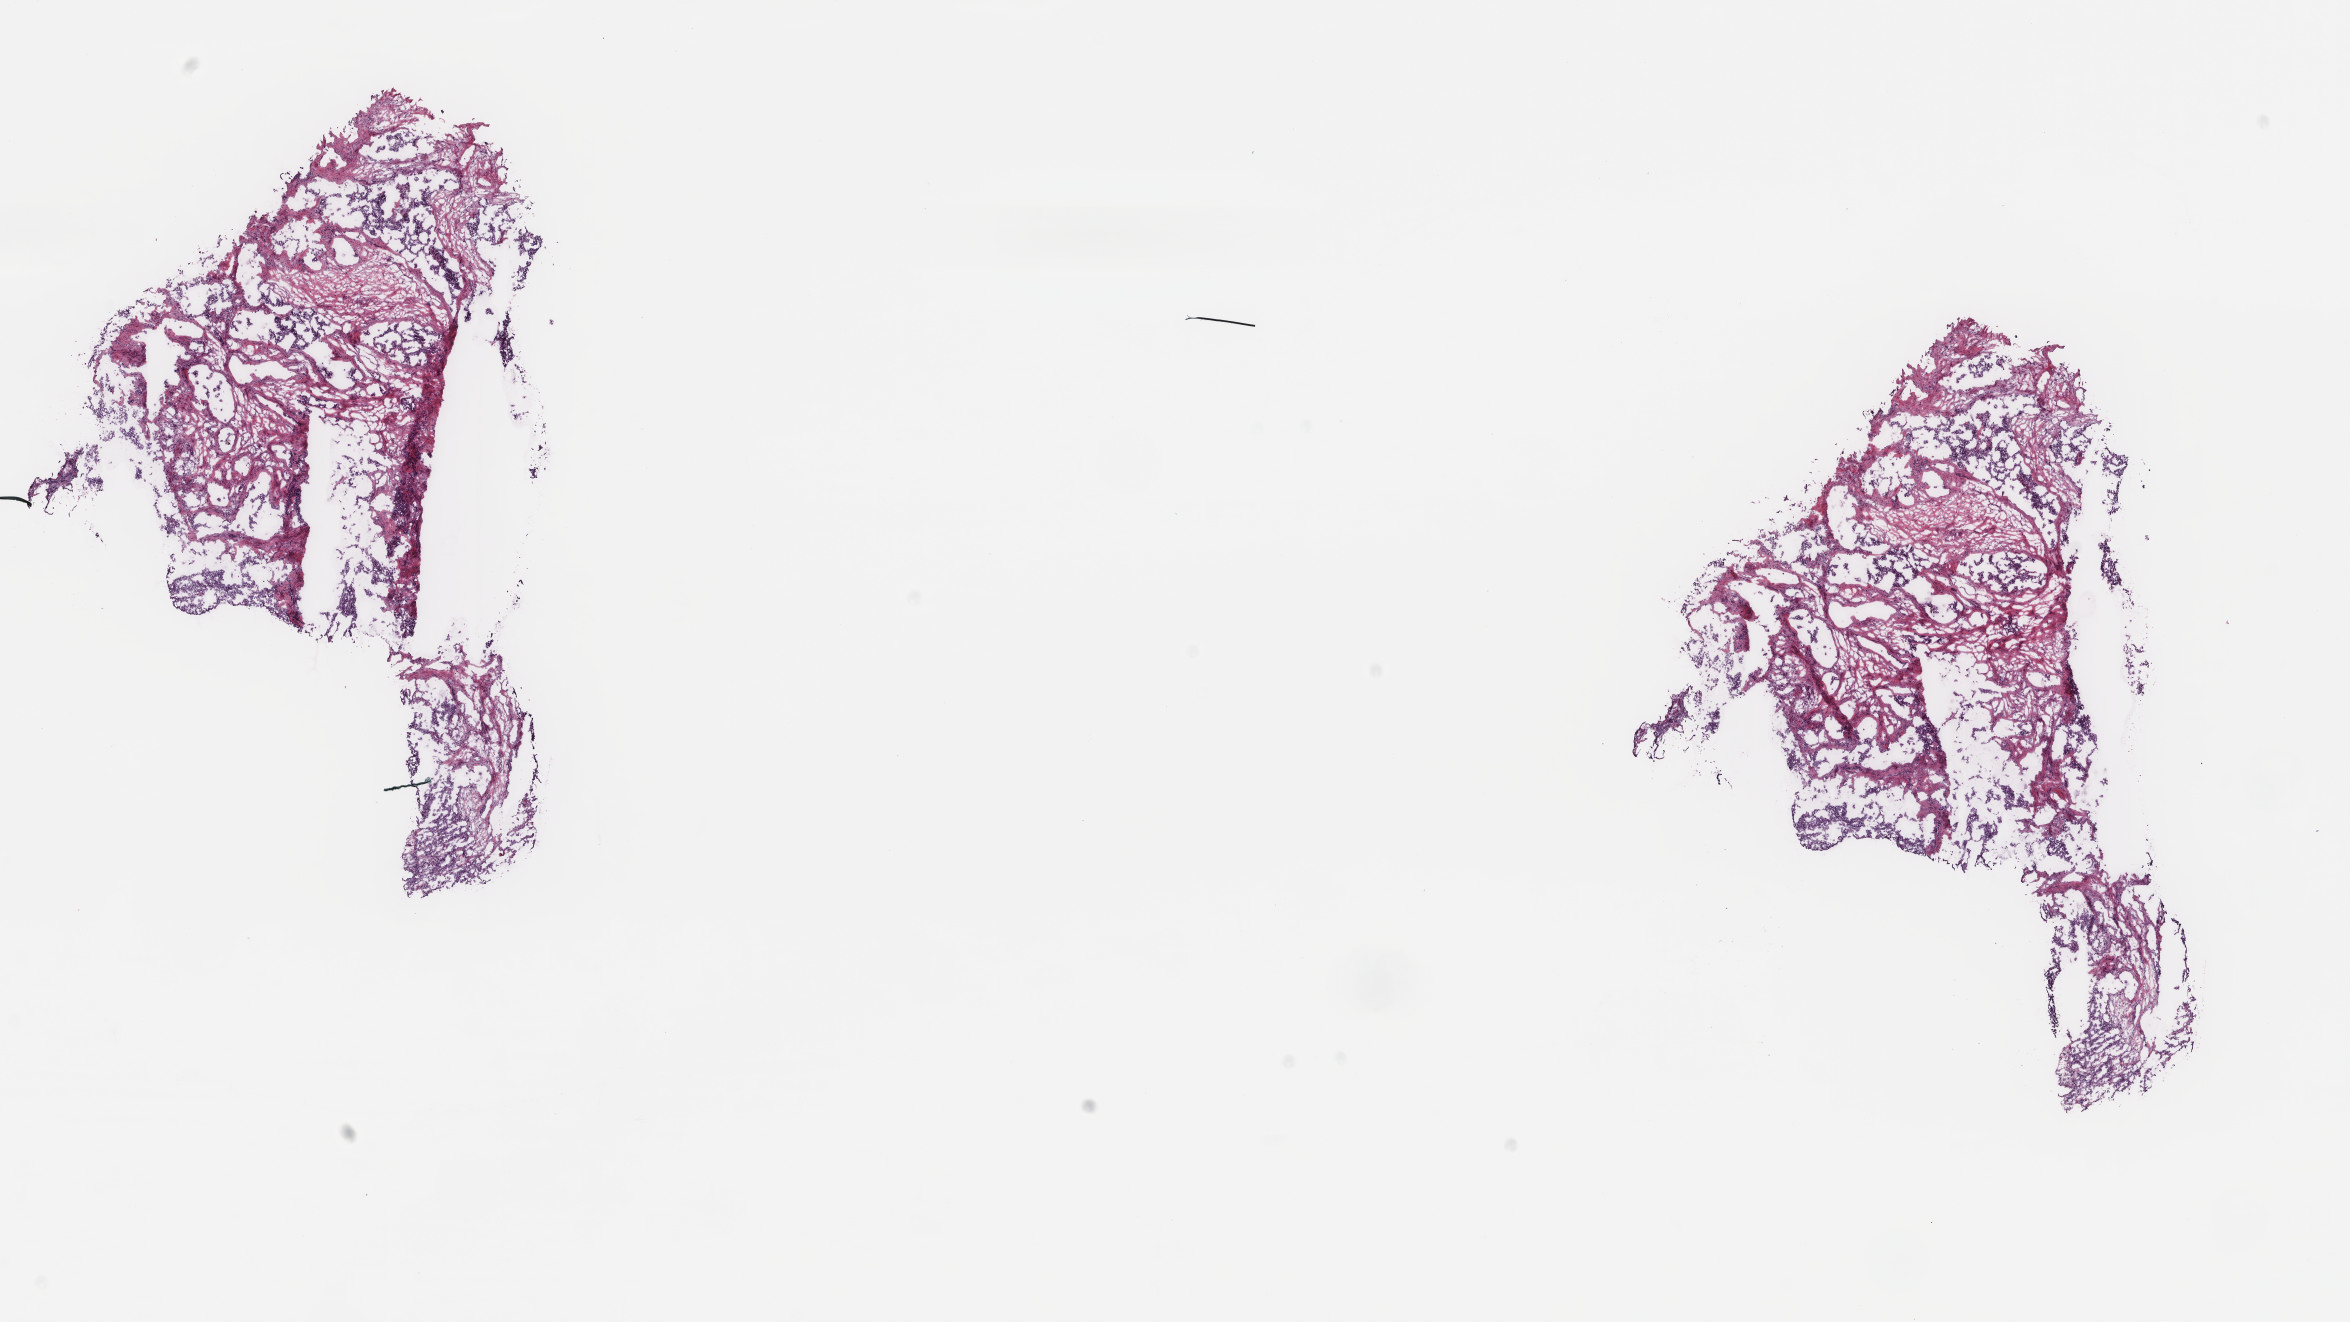
Digitized H&E tissue section (whole slide), whole scanned area (about 18.7 x 10.5 mm) shown as a low-resolution overview, frozen section, sample: primary tumour, thyroid. Female patient; age at initial diagnosis 69 years. Composition of this section per pathologist review: tumour cells 80%, tumour nuclei 80%, normal cells 0%, stromal cells 20%, necrosis 0%. Infiltration values recorded for this section: lymphocyte infiltration 0%, monocyte infiltration 0%, neutrophil infiltration 0%.
• AJCC pathologic stage: IV (6th edition)
• laterality: left
• diagnosis: Papillary adenocarcinoma, NOS (thyroid gland)
• TNM: T4 N1 MX